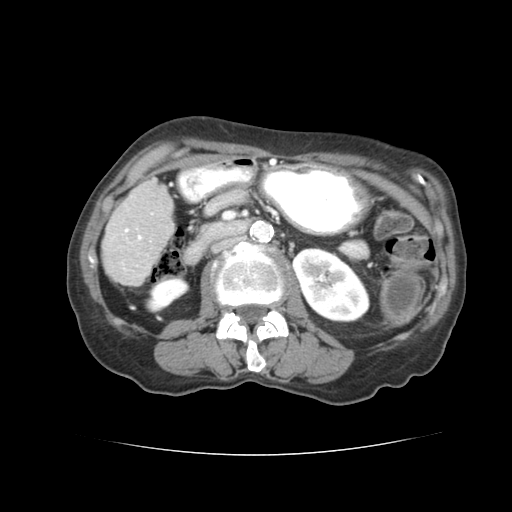
Contrast-enhanced abdominal CT (liver protocol), one axial slice; slice 17 of 77 in the series (ordered by position); 120 kVp; soft-tissue window (W 400 / L 40 HU); 2.5 mm slice thickness; 512 × 512 image matrix, field of view 340 × 340 mm. Case-level facts recorded for this patient, not image findings: diagnosis: hepatocellular carcinoma (patient treated with transarterial chemoembolisation; whether this scan precedes or follows treatment is not stated here); TNM stage (as recorded): Stage-I; Child-Pugh class: A; tumour size: 7.6 cm.
Outlined on this slice (semi-automatic segmentation, software-assisted and operator-edited):
- liver parenchyma outside the tumour (the mass and vessels are separate outlines, so this box may not span the whole liver): bounding box <102,178,170,282> (left, top, right, bottom; pixels)
- liver vessels: <134,220,151,240>